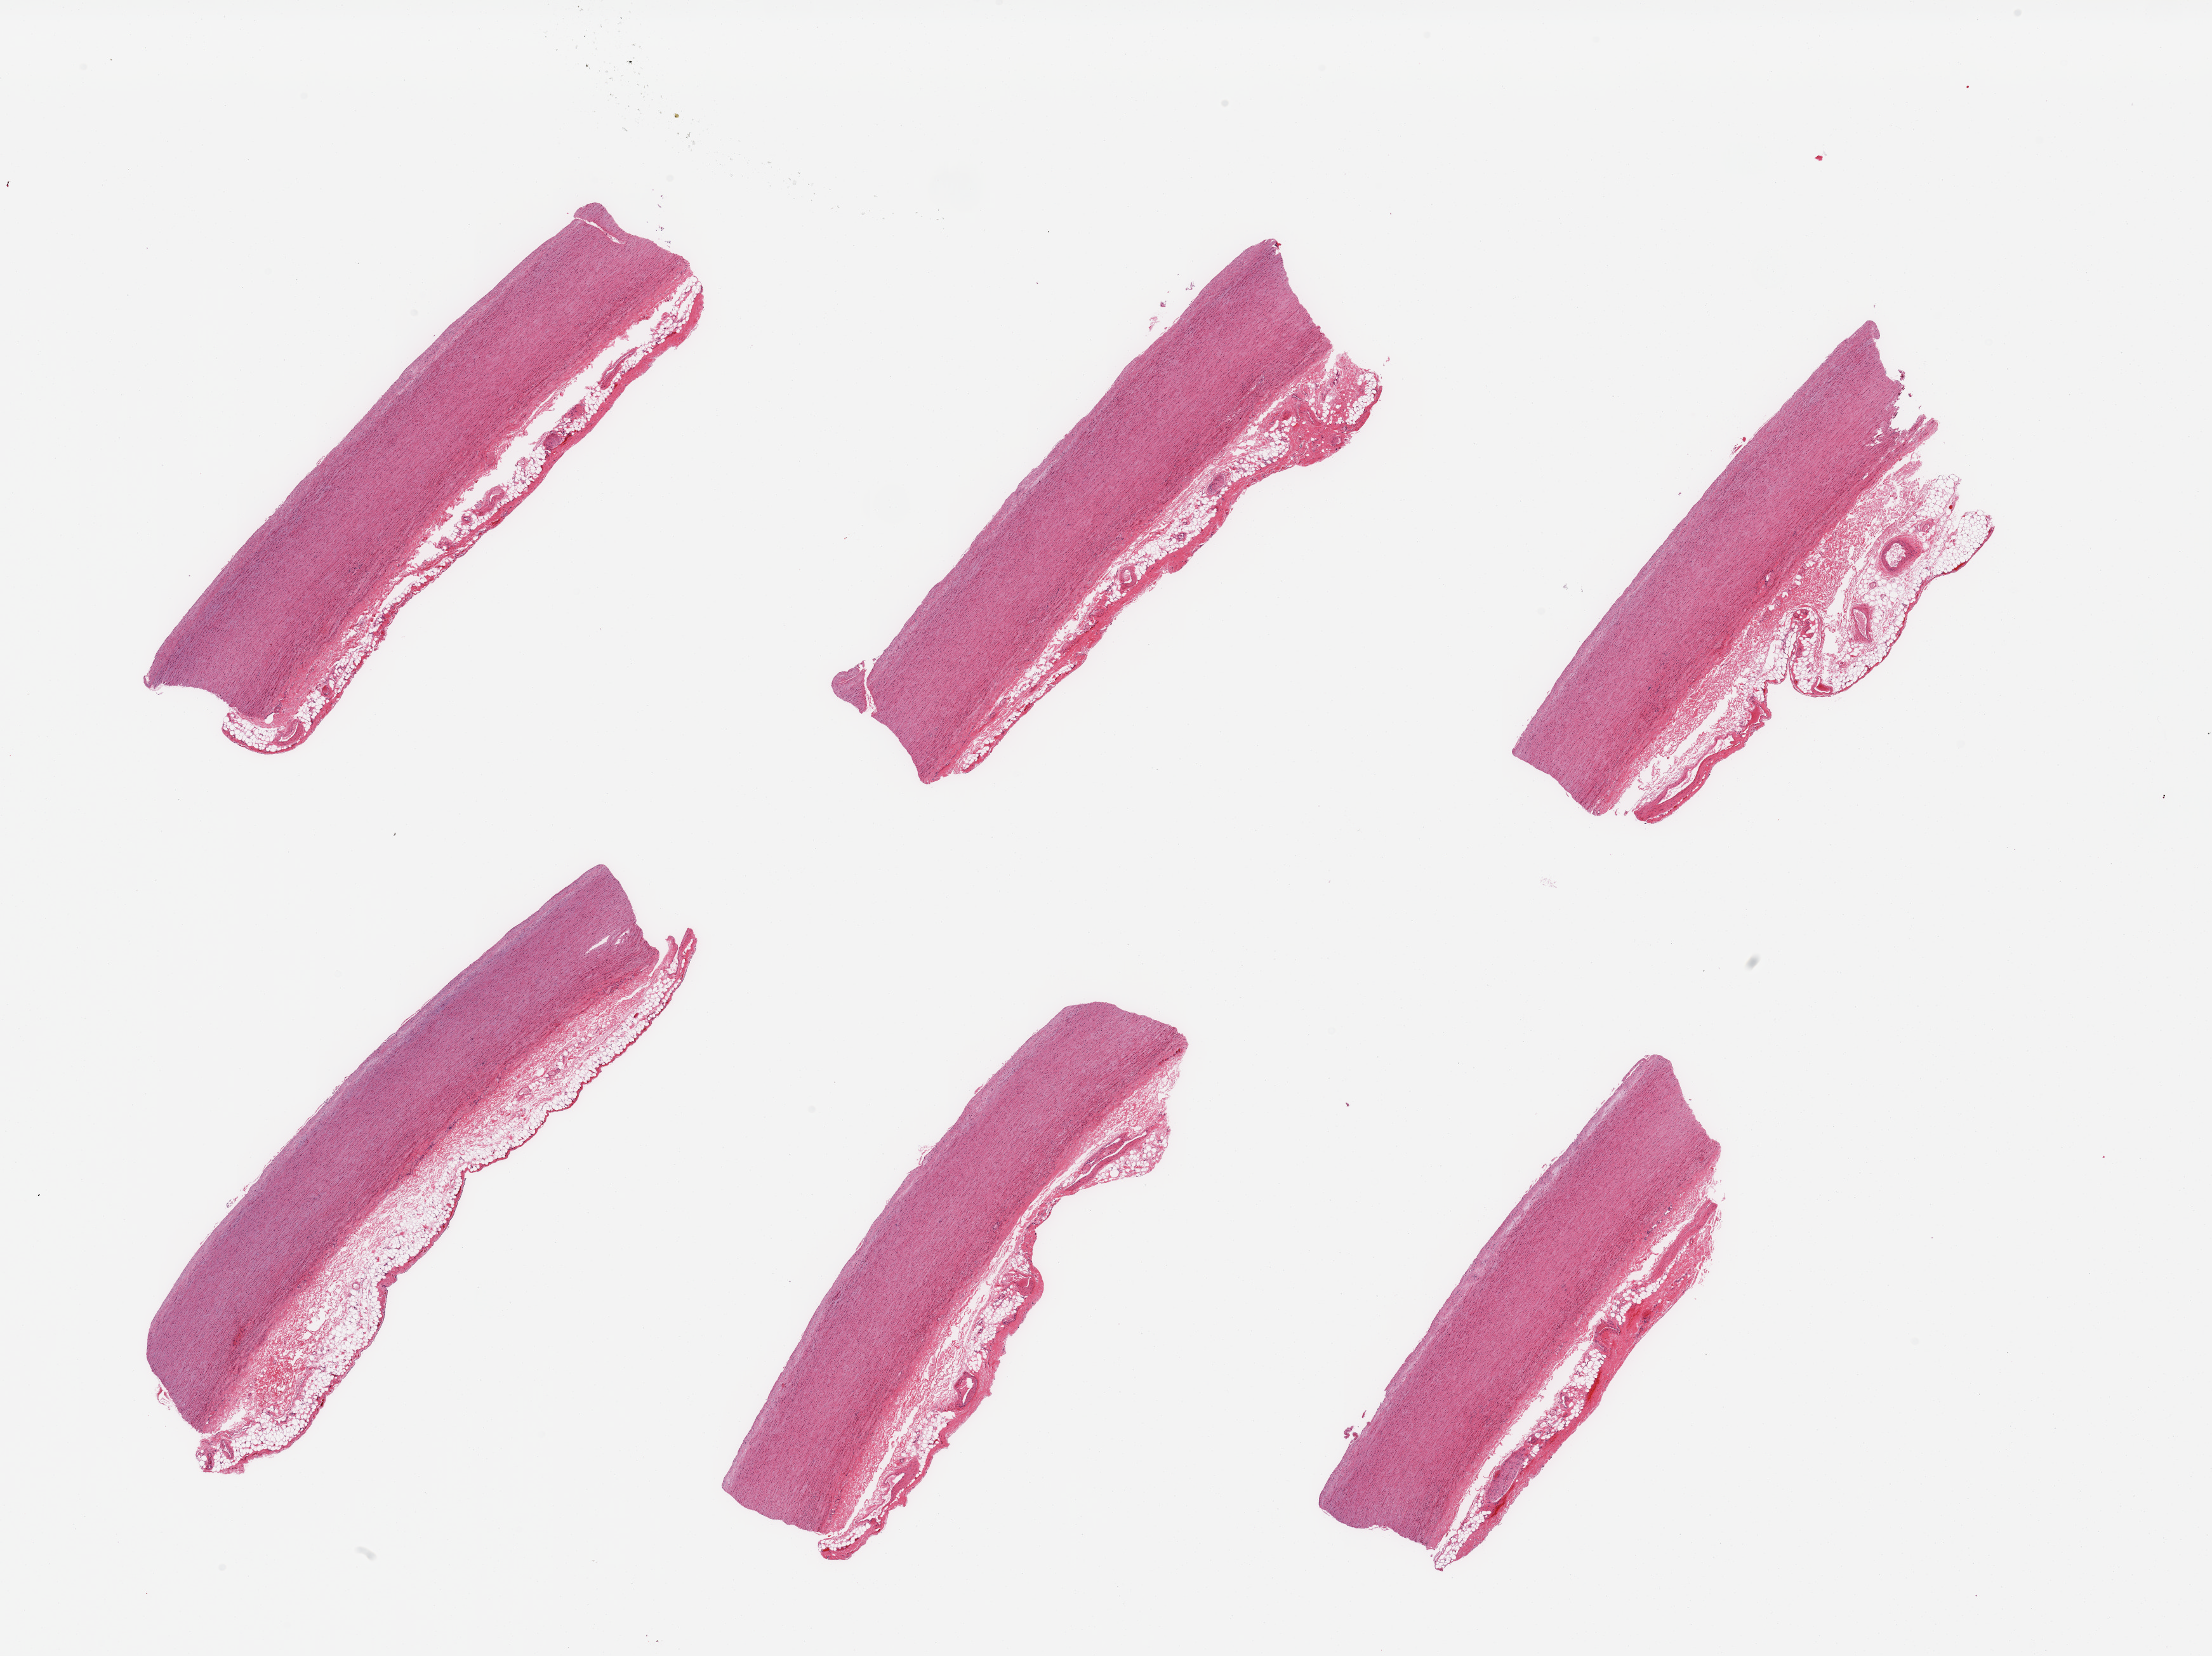
H&E whole-slide image, brightfield — whole scanned area (about 27.6 x 20.6 mm, slide scanned at 20x) shown as a low-resolution overview; PAXgene-fixed, paraffin-embedded tissue; sampled site (target tissue): aorta; tissue donor sample. Donor sex: male.
Review note (as recorded): 6 pieces; minimal intimal thickening; adventitia up to 1.4mm thick on all.